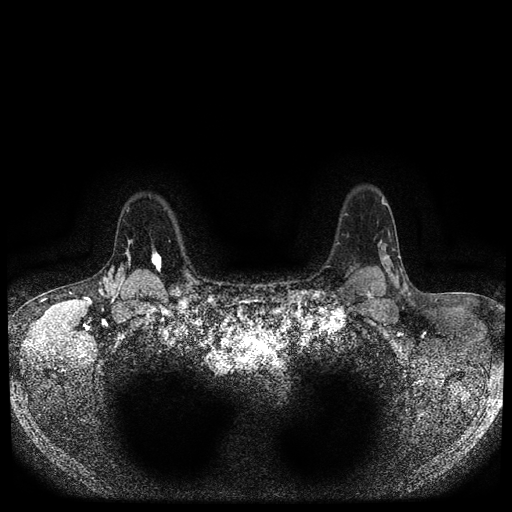
Breast MRI (dynamic contrast-enhanced, multi-phase), one axial slice; slice 81 of 116 in the series (ordered by position); dynamic contrast-enhanced series, time point 2 of 5 at this slice position (early post-contrast); 1.5 T; TE 2.6 ms, TR 5.4 ms; 2 mm slice thickness; 512 × 512 image matrix, field of view 340 × 340 mm. Female patient, age 47 years.
Structures marked on this image (semi-automatic segmentation, software-assisted and operator-edited):
- breast lesion (labelled 'tumour' in the annotation; benign lesions carry a separate 'benign' label): bounding box <150,247,162,277> (left, top, right, bottom; pixels)